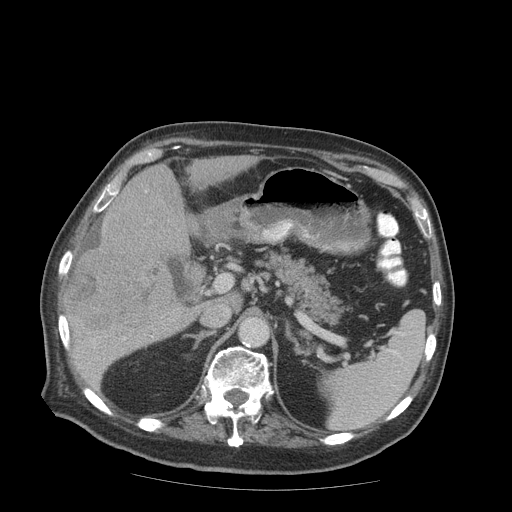
Contrast-enhanced abdominal CT (liver protocol), one axial slice; slice 47 of 99 in the series (ordered by position); 140 kVp; soft-tissue window (W 400 / L 40 HU); 2.5 mm slice thickness; 512 × 512 image matrix, field of view 420 × 420 mm. Case-level facts recorded for this patient, not image findings: diagnosis: hepatocellular carcinoma (patient treated with transarterial chemoembolisation; whether this scan precedes or follows treatment is not stated here); TNM stage (as recorded): Stage-IIIB; Child-Pugh class: A.
Outlined on this slice (semi-automatically segmented with operator editing):
- liver parenchyma outside the tumour (the mass and vessels are separate outlines, so this box may not span the whole liver): bounding box <66,156,256,387> (left, top, right, bottom; pixels)
- mass: <64,200,187,334>